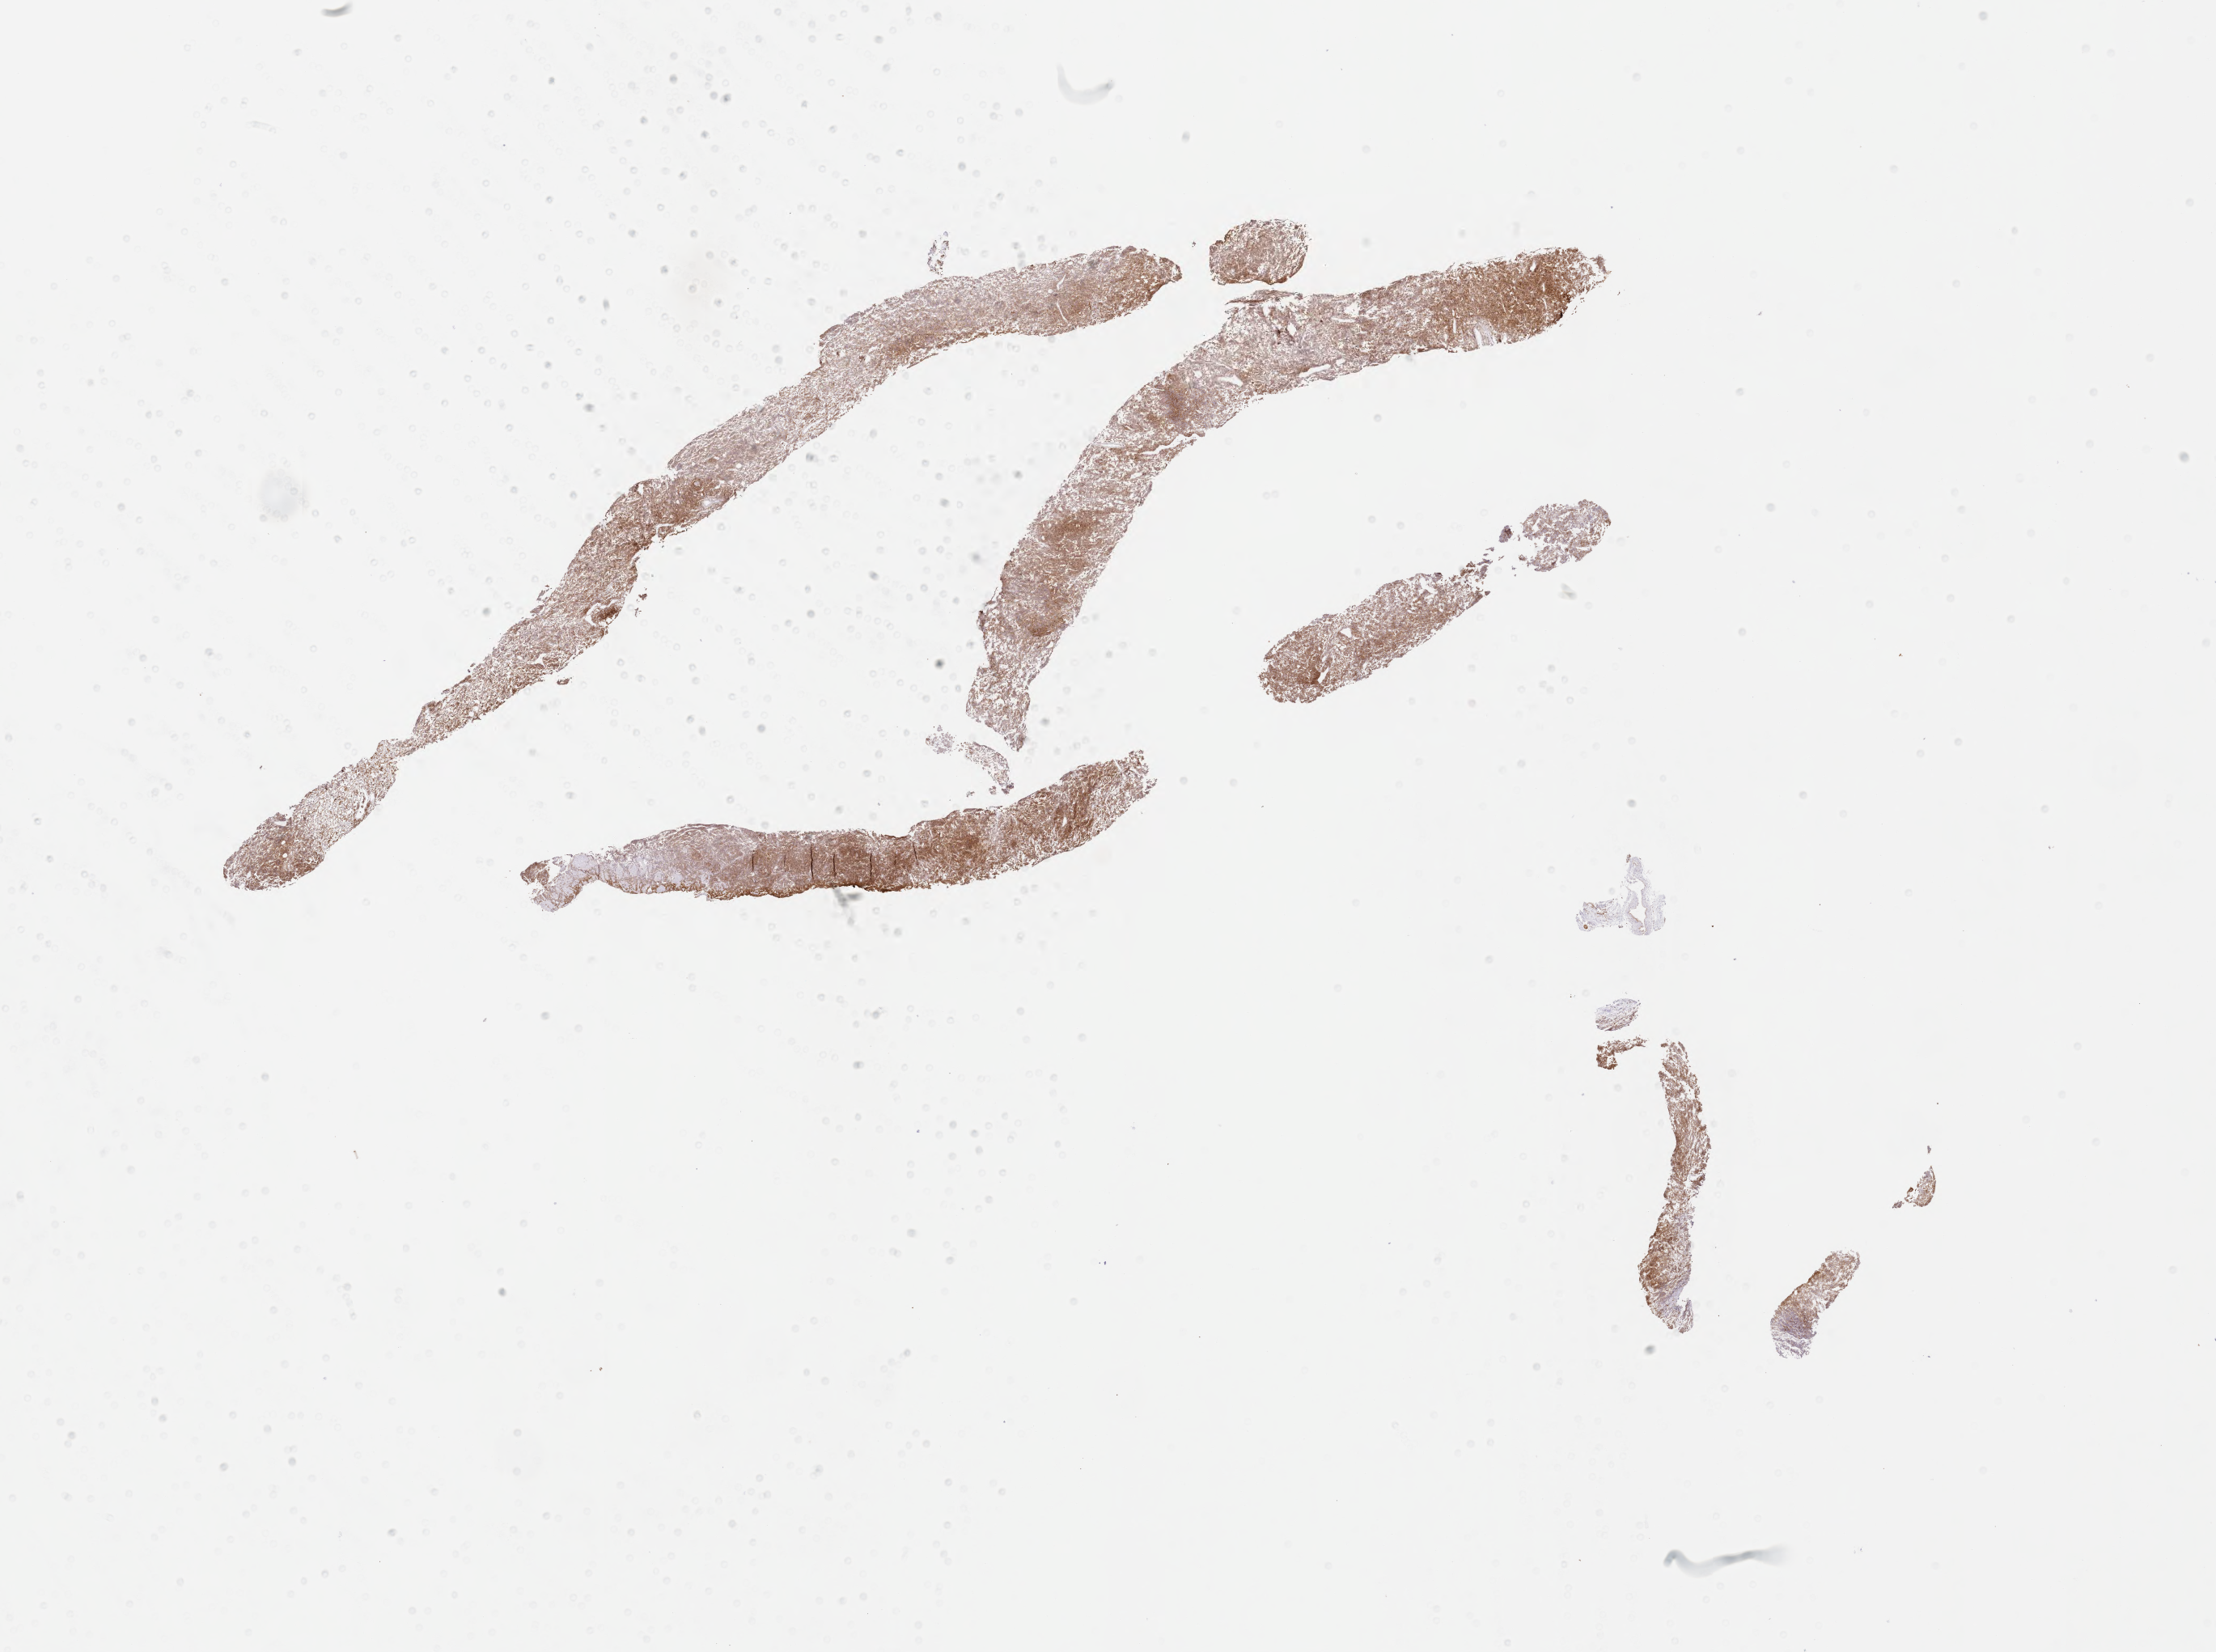
Whole-slide image, immunohistochemical stain for CD10, low-resolution overview of the scanned area, about 22.1 x 16.5 mm. Specimen: tumor tissue. Male patient, aged 66.
* diagnosis: Burkitt lymphoma, NOS